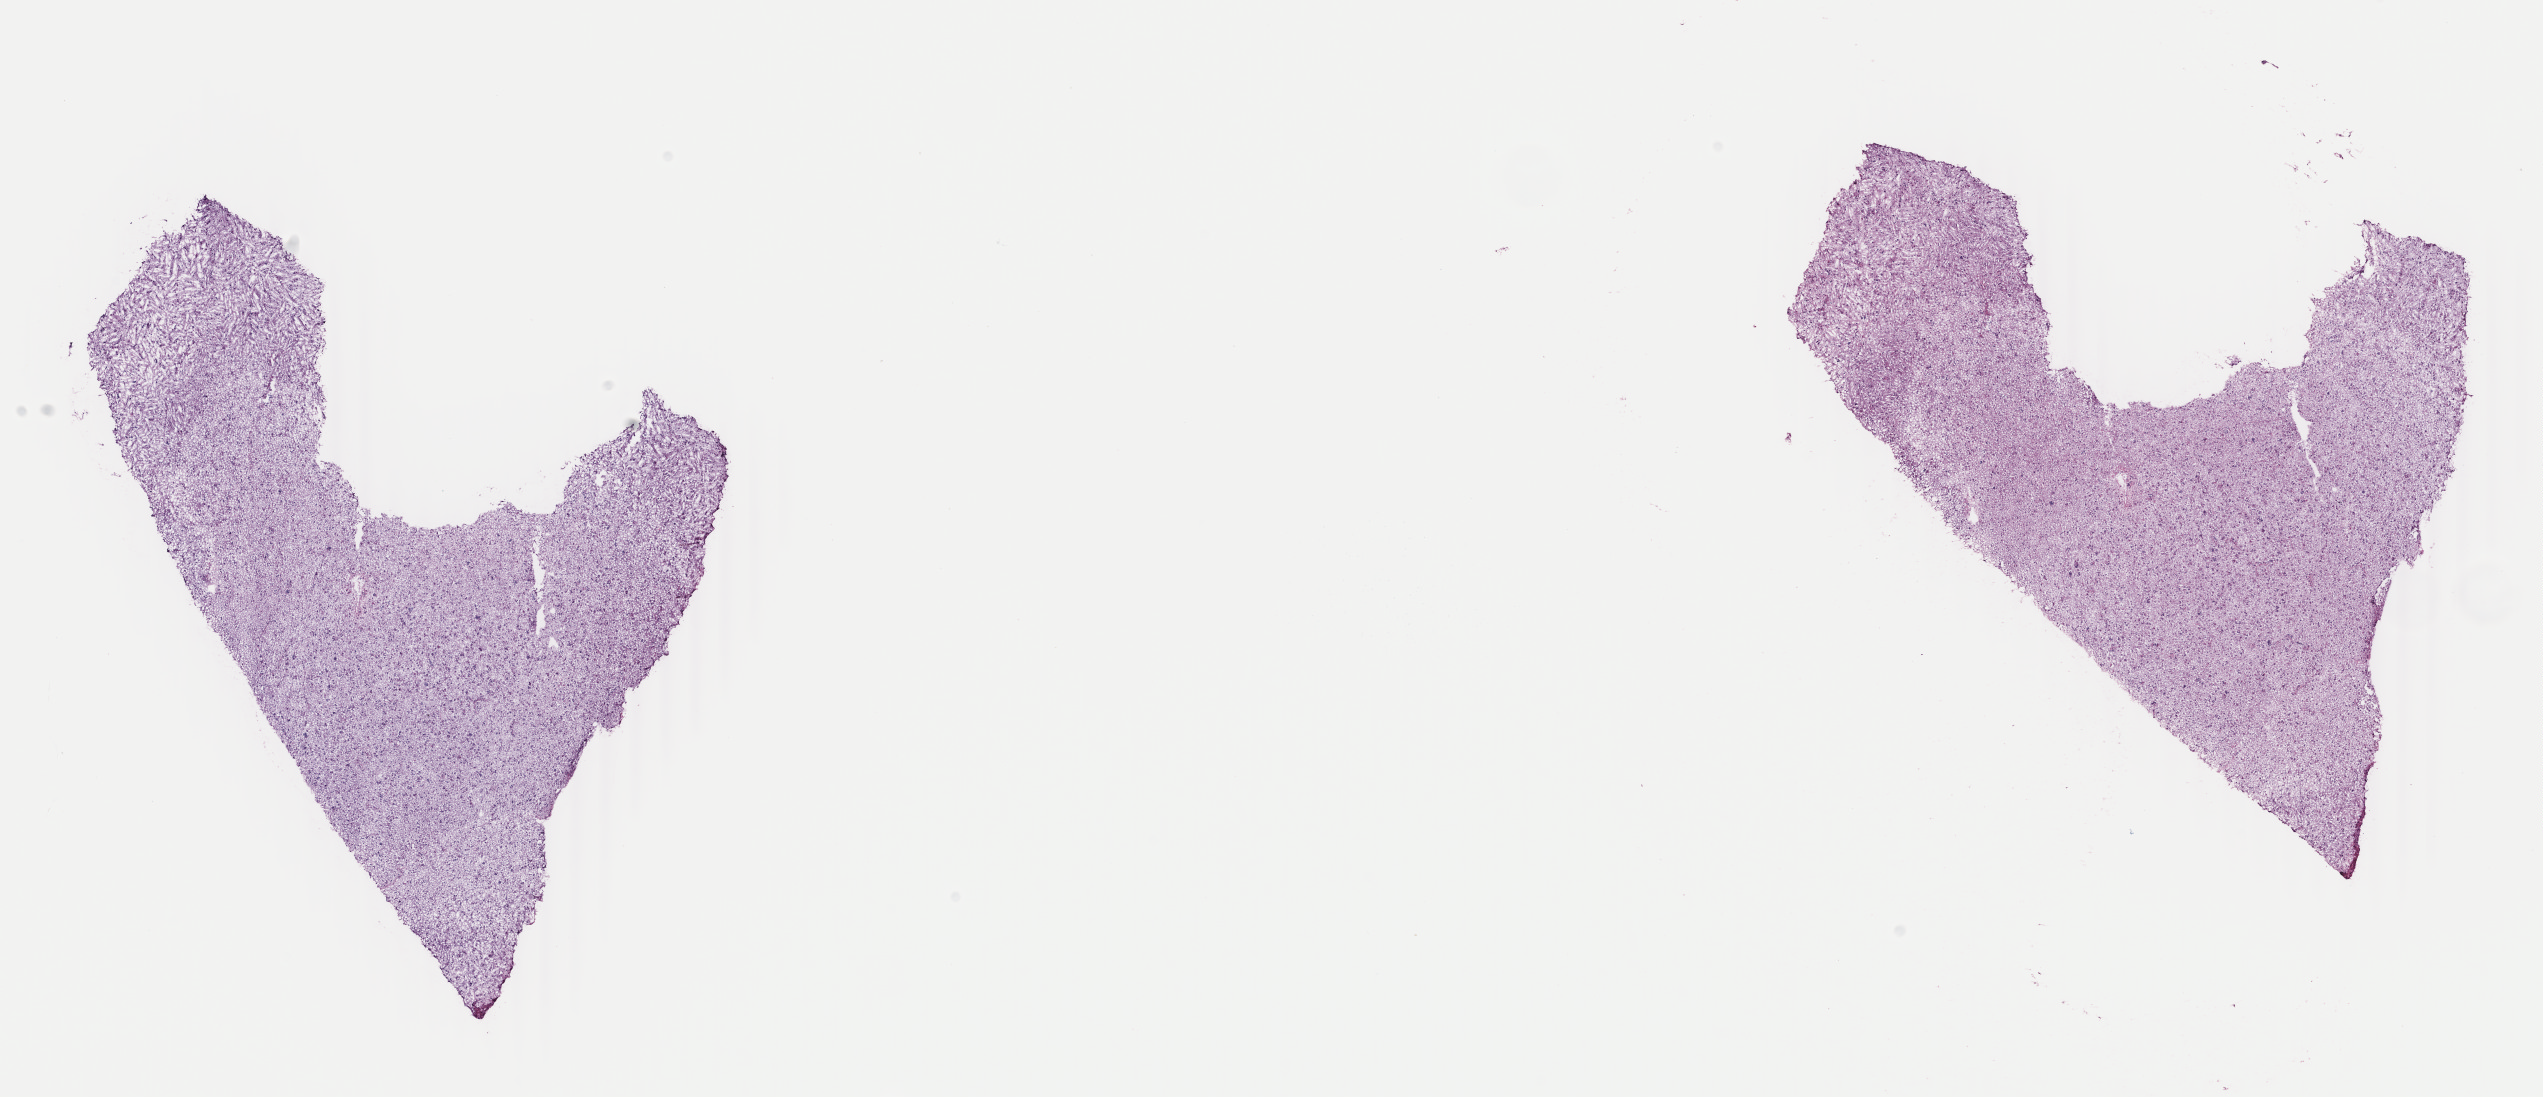
H&E whole-slide image, whole scanned area (about 20.2 x 8.7 mm) shown as a low-resolution overview, frozen section from the top of the tissue portion, brain, primary tumour sample. Female patient; age at initial diagnosis 36 years. Histologic grade: G3 (poorly differentiated). Slide review estimates, as recorded: tumour cells 40%, tumour nuclei 90%, normal cells 10%, stromal cells 50%, necrosis 0%. Inflammatory infiltration, as recorded: lymphocyte infiltration 0%, monocyte infiltration 0%, neutrophil infiltration 0%.
- histologic diagnosis: Astrocytoma, anaplastic (cerebrum)
- laterality: right